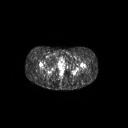
FDG PET of an extremity soft-tissue mass (from a PET/CT study), one axial slice. Slice 35 of 267 in the series (ordered by position). 3.27 mm slice thickness. 128 × 128 image matrix. Patient: female, 17 years. From the clinical record (not read from this slice): histological type: epithelioid sarcoma; grade: intermediate; site of the primary tumour: right buttock.
Annotated regions visible in this slice (expert contour drawn on MRI and transferred to this co-registered scan by the dataset authors):
- gross tumour volume including surrounding oedema: bounding box <50,71,57,79> (left, top, right, bottom; pixels)
- gross tumour volume (mass): <51,72,56,78>